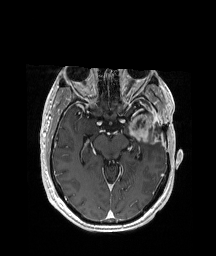
Brain MRI from a brain-tumour surgery series, one axial slice; position 121 of 208 along the scan axis; T1-weighted post-contrast; 1 mm slice thickness; 216 × 256 image matrix, field of view 228 × 270 mm. From the clinical record (not read from this slice): histopathology: Glioblastoma; WHO grade: 4; IDH mutation: no; tumour location: Left Anterior/Superior Temporal.
Structures marked on this image (outlined manually by an expert reader):
- previous resection cavity: bounding box (x1, y1, x2, y2) in pixels: (135, 118, 161, 133)
- tumour: (130, 112, 157, 140)